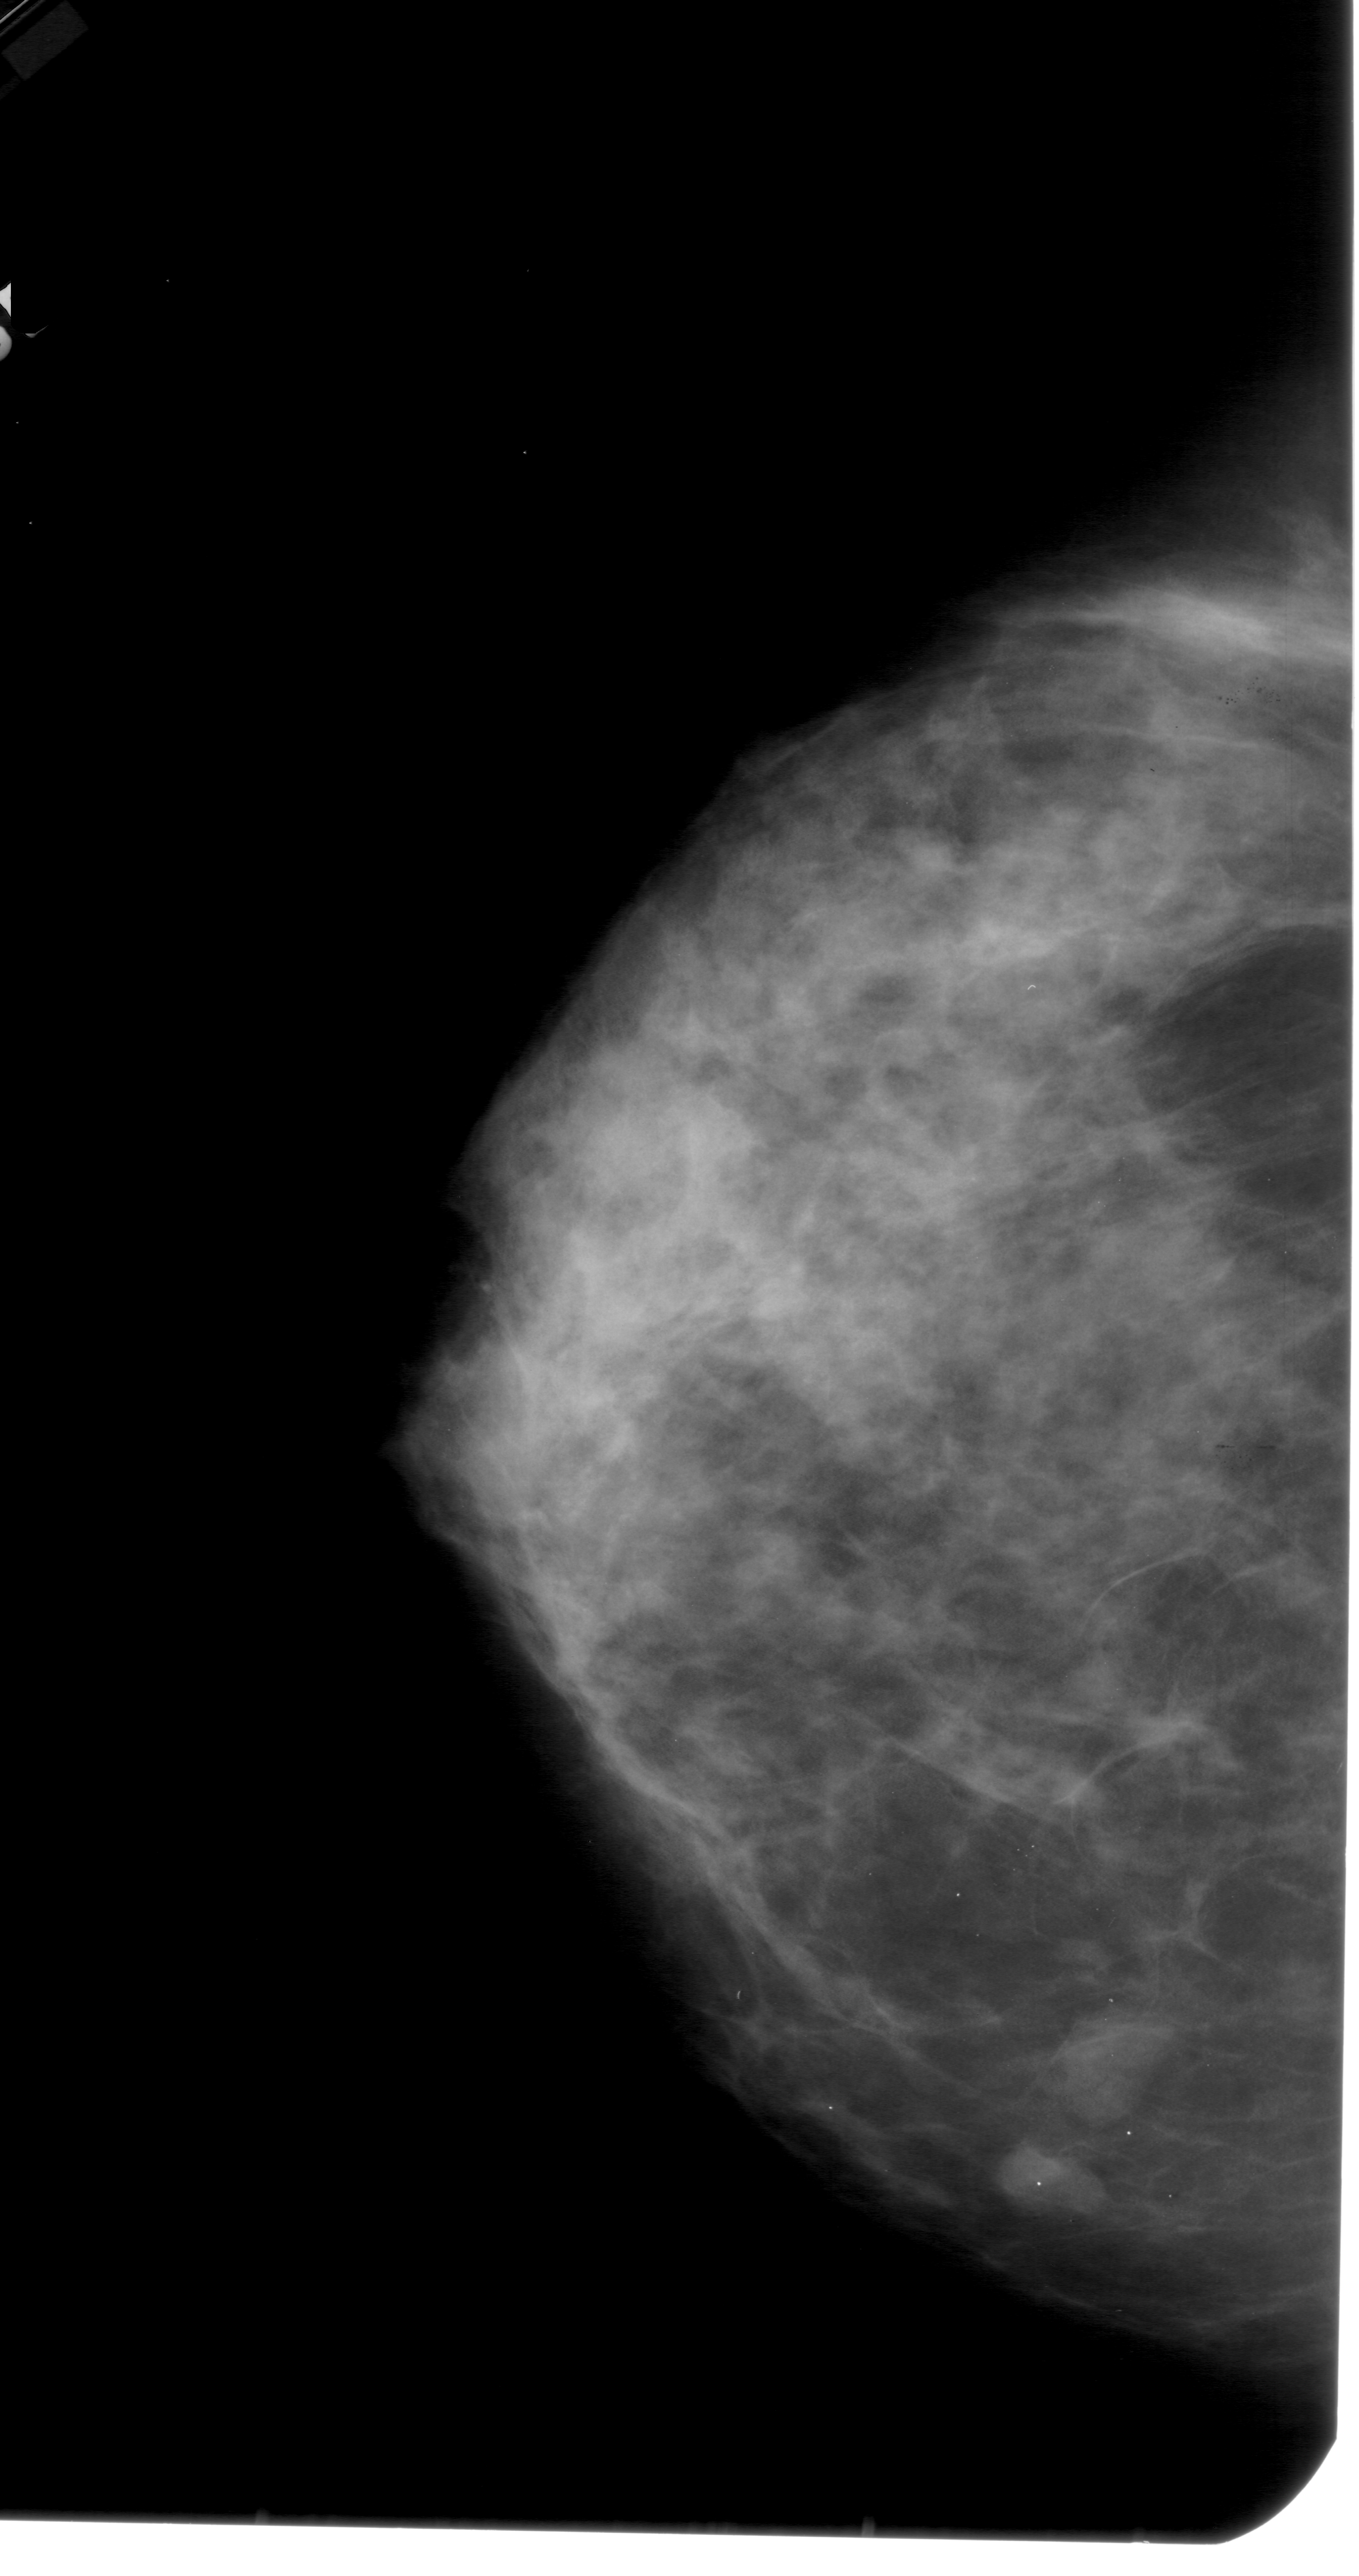
Digitized screen-film mammogram; left breast; craniocaudal (CC) view; breast composition: heterogeneously dense (BI-RADS density category 3 of 4); 1359 × 2576 image matrix.
Expert-marked regions of interest on this image (one box per marked abnormality):
- mass, shape lobulated, margins circumscribed; BI-RADS assessment category 4; pathology (as recorded): benign: bounding box (x1, y1, x2, y2) in pixels: (983, 2104, 1110, 2227)